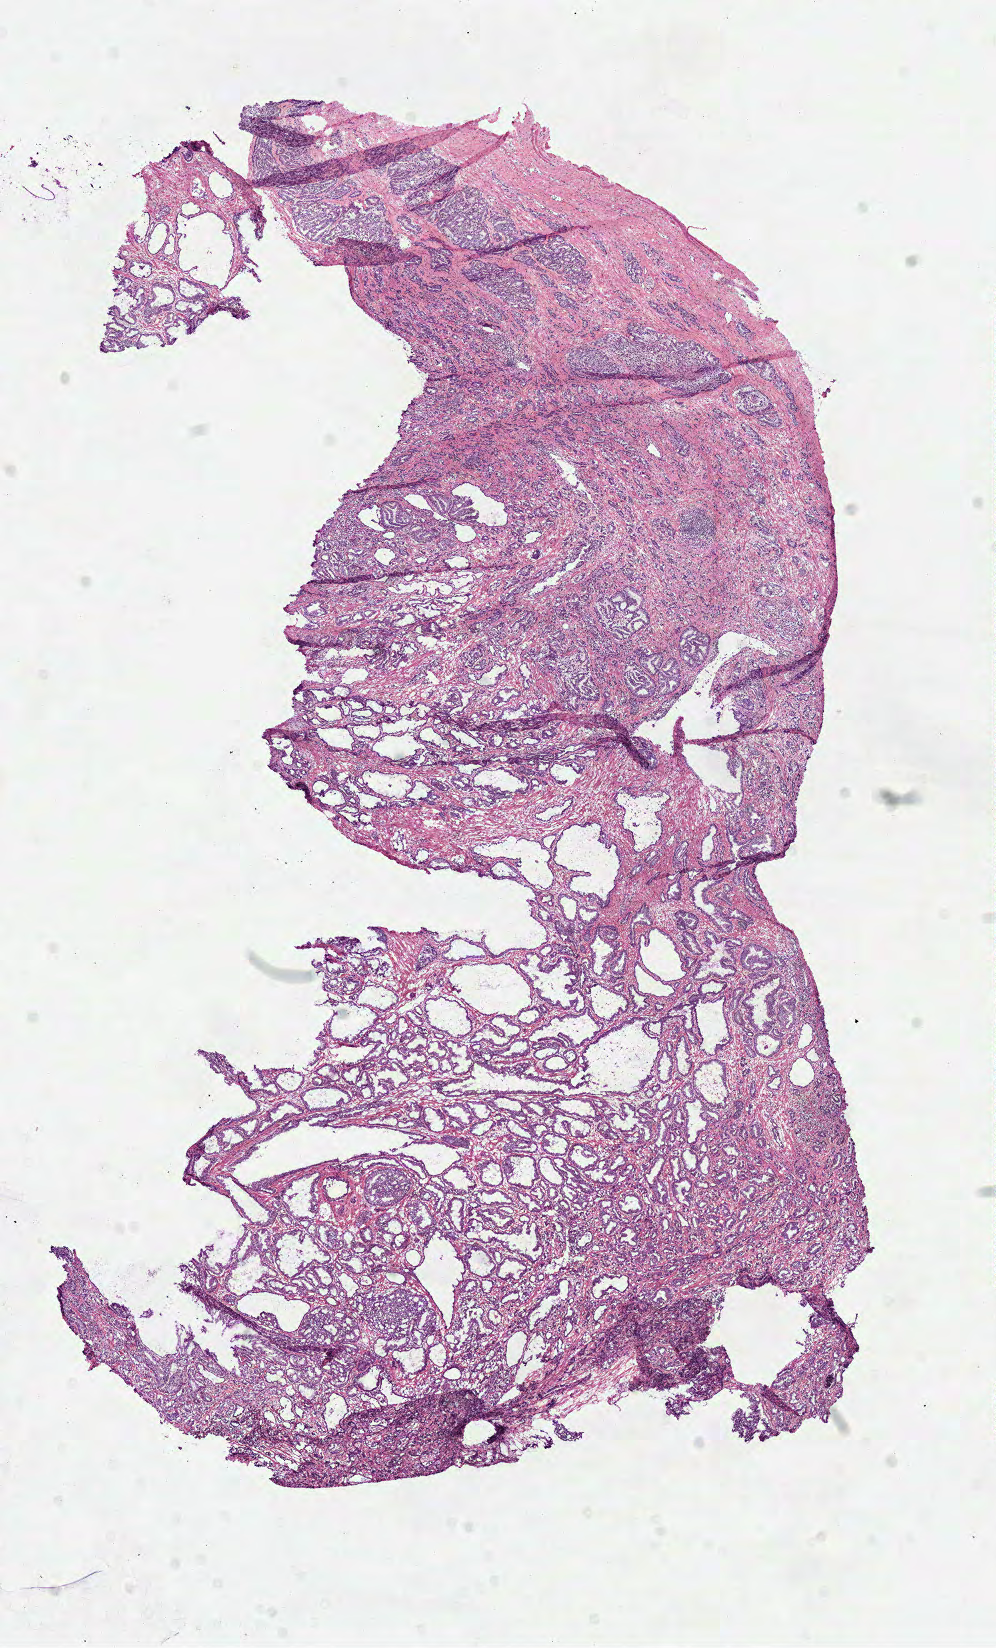
H&E-stained whole-slide image, low-resolution overview of the scanned area, about 7.8 x 13.0 mm (from a 40x scan); frozen section from the top of the tissue portion; sample: primary tumour, prostate. Male, age 60 years at initial diagnosis. Gleason score: 9 (4+5). Pathologist review of this section (percent, as recorded): tumour cells 60%, tumour nuclei 65%, normal cells 25%, stromal cells 15%, necrosis 0%. Infiltration values recorded for this section: lymphocyte infiltration 5%, monocyte infiltration 0%, neutrophil infiltration 0%.
Histologic diagnosis: Acinar cell carcinoma (prostate gland).